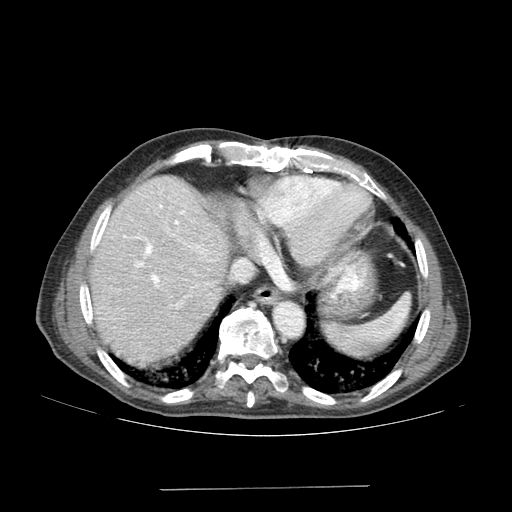
Contrast-enhanced abdominal CT (liver protocol), one axial slice. Slice 144 of 192 in the series (ordered by position). Reconstruction kernel SOFT. Soft-tissue window (W 400 / L 40 HU). 2.5 mm slice thickness. 512 × 512 image matrix, field of view 400 × 400 mm. From the clinical record (not read from this slice): diagnosis: hepatocellular carcinoma (patient treated with transarterial chemoembolisation; whether this scan precedes or follows treatment is not stated here); TNM stage (as recorded): Stage-IVA; Child-Pugh class: A; tumour differentiation: poorly differentiated.
Annotated regions visible in this slice (semi-automatic segmentation, software-assisted and operator-edited):
- liver parenchyma outside the tumour (the mass and vessels are separate outlines, so this box may not span the whole liver): bounding box (x1, y1, x2, y2) in pixels: (90, 176, 228, 366)
- liver vessels: (124, 205, 212, 306)